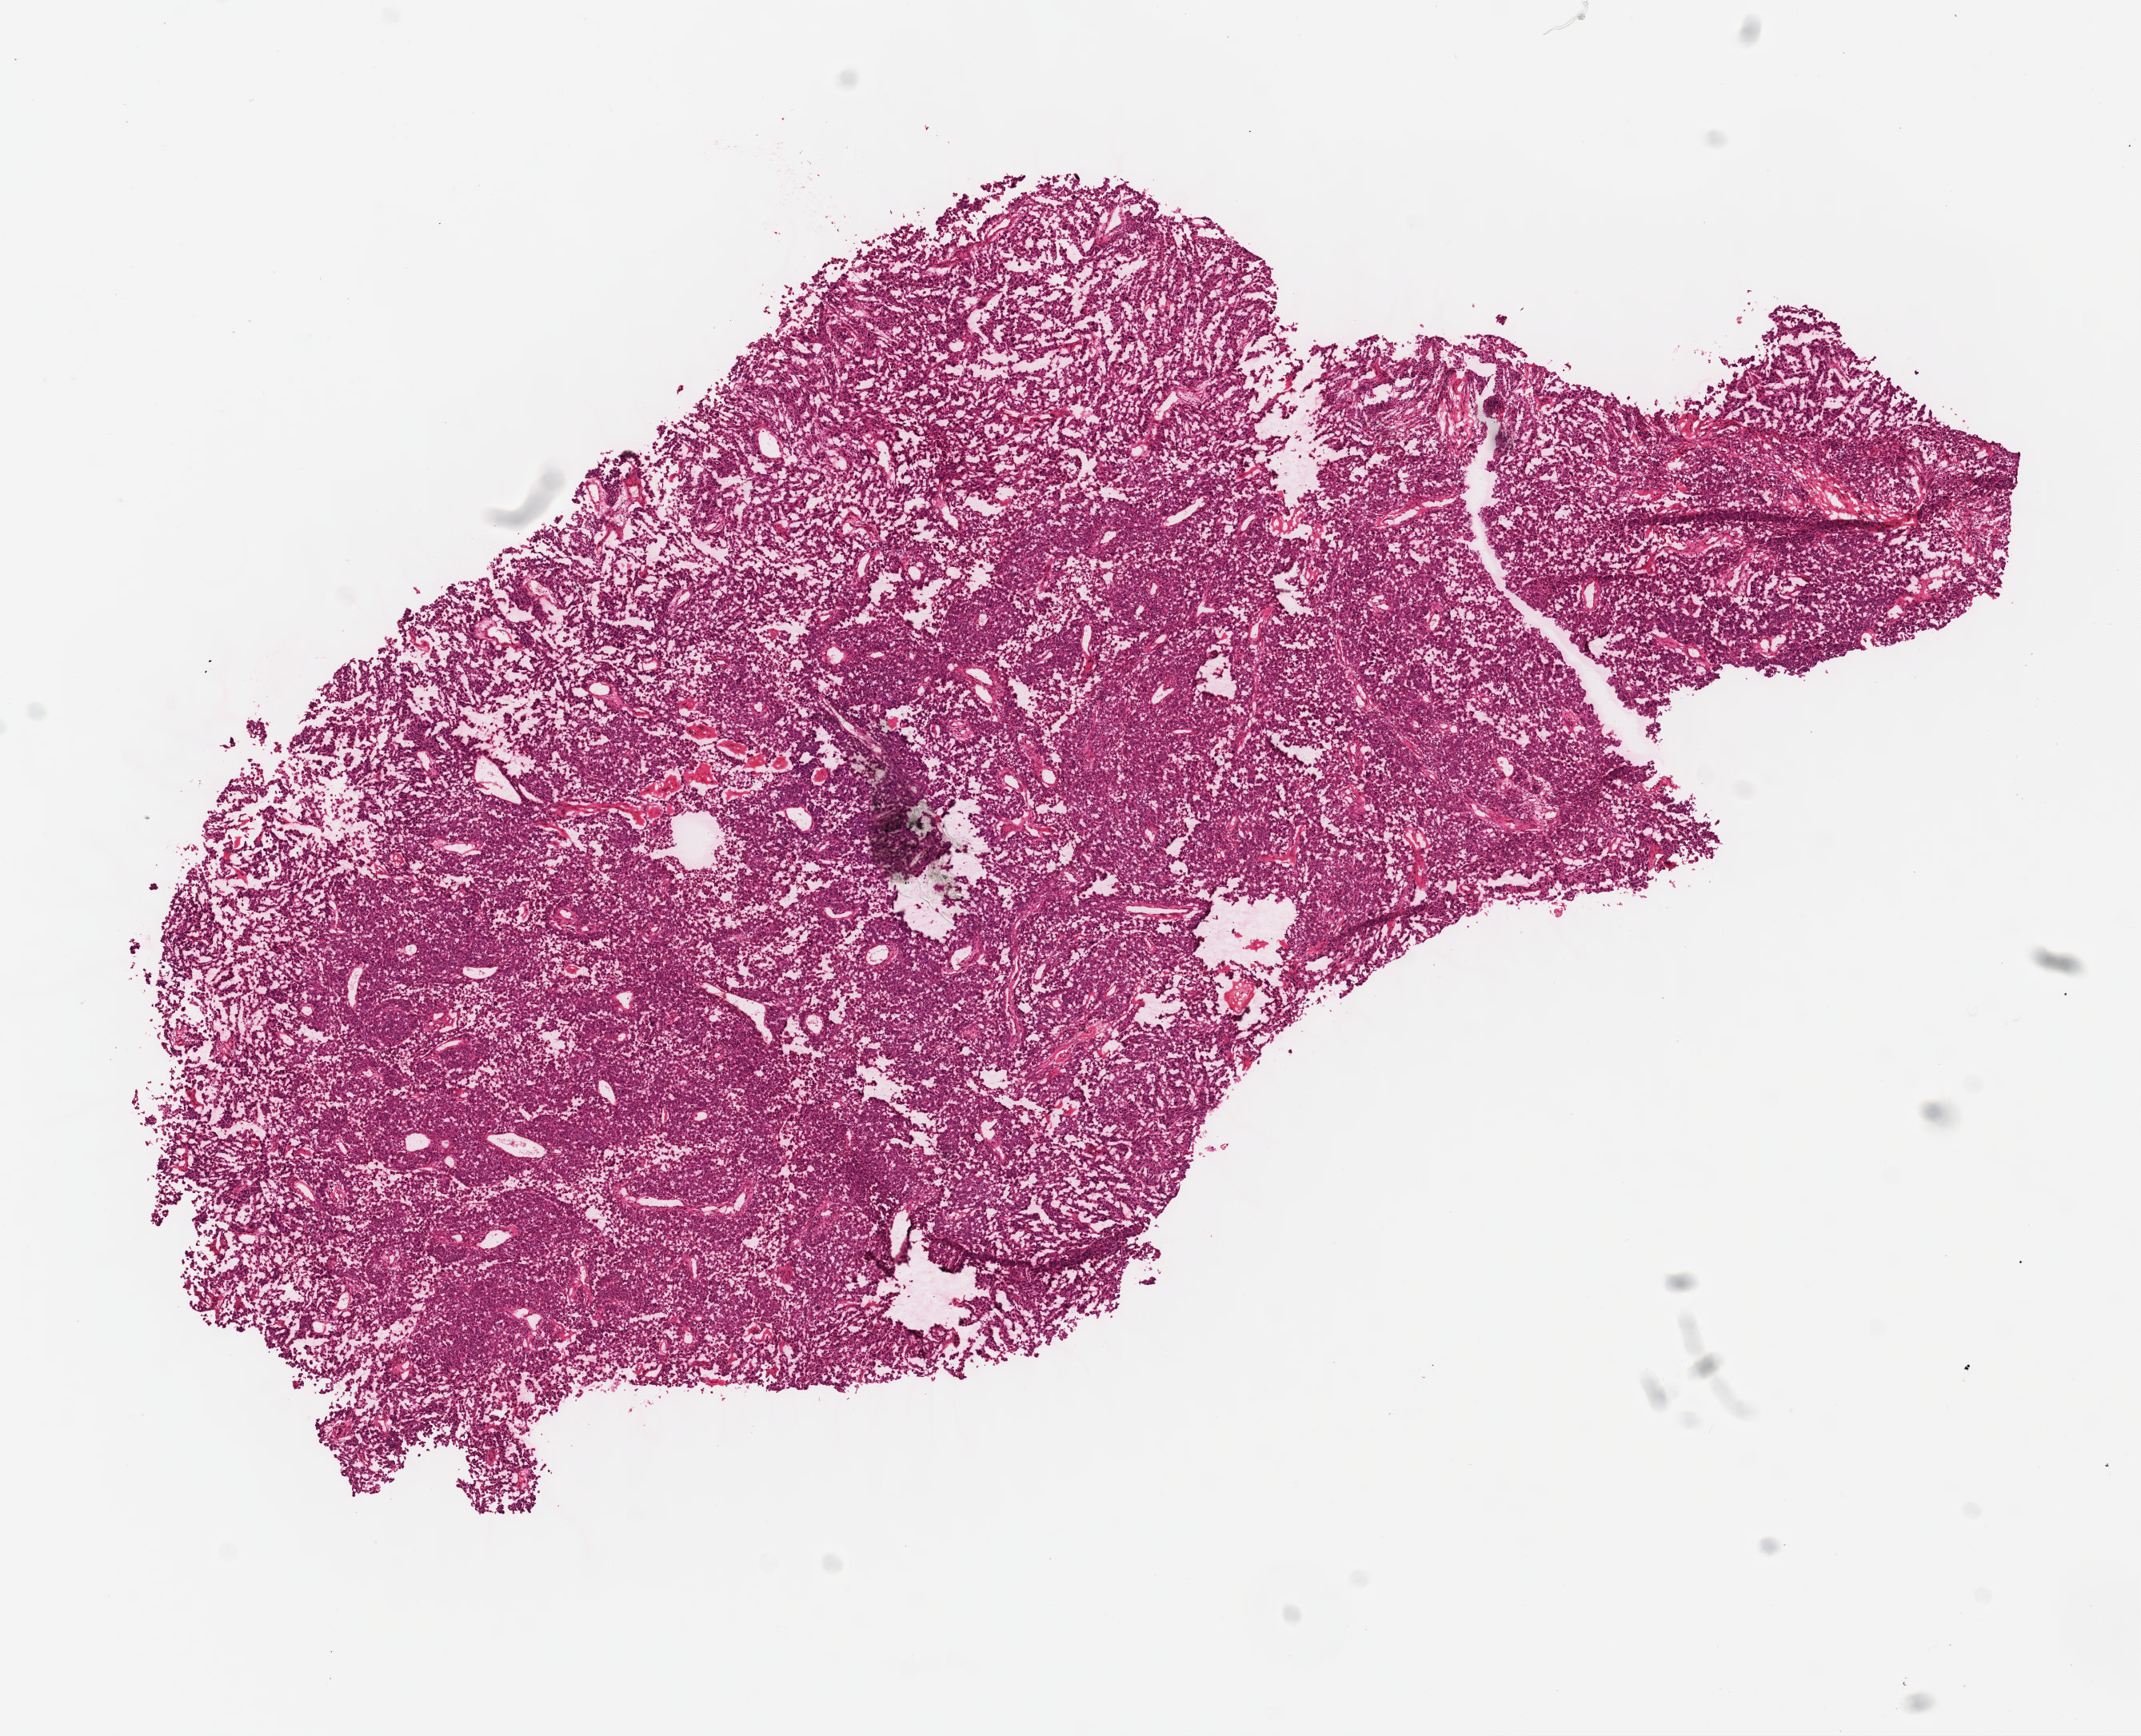
H&E whole-slide image, shown as a low-resolution overview of the whole scanned area (about 10.5 x 8.5 mm, slide scanned at 40x). Formalin-fixed paraffin-embedded (FFPE) diagnostic section. Skin, primary tumour sample. Patient: male, age at initial diagnosis 75 years.
Pathologic diagnosis: Malignant melanoma, NOS.